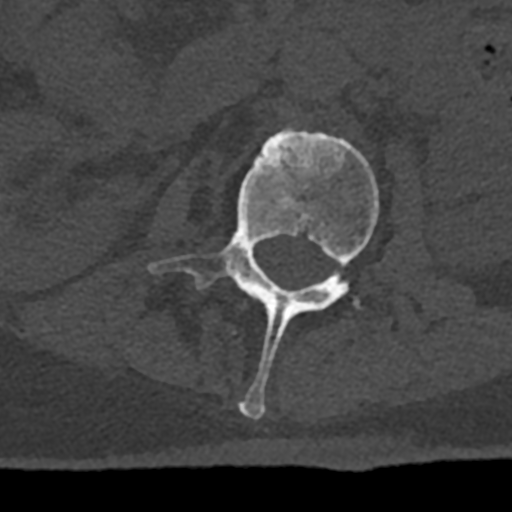
CT including the spine, one axial slice; slice 376 of 797 in the series (ordered by position); 120 kVp; bone window (W 1800 / L 400 HU); 512 × 512 image matrix, field of view 160 × 160 mm. Patient: male, 74 years. Case-level facts recorded for this patient, not image findings: primary cancer: renal; vertebrae with lytic lesions (as recorded): T10, L1, L2, L3, L4, L5.
Annotated regions visible in this slice (semi-automatic segmentation, software-assisted and operator-edited):
- L2 vertebra: bounding box <148,128,379,419> (left, top, right, bottom; pixels)